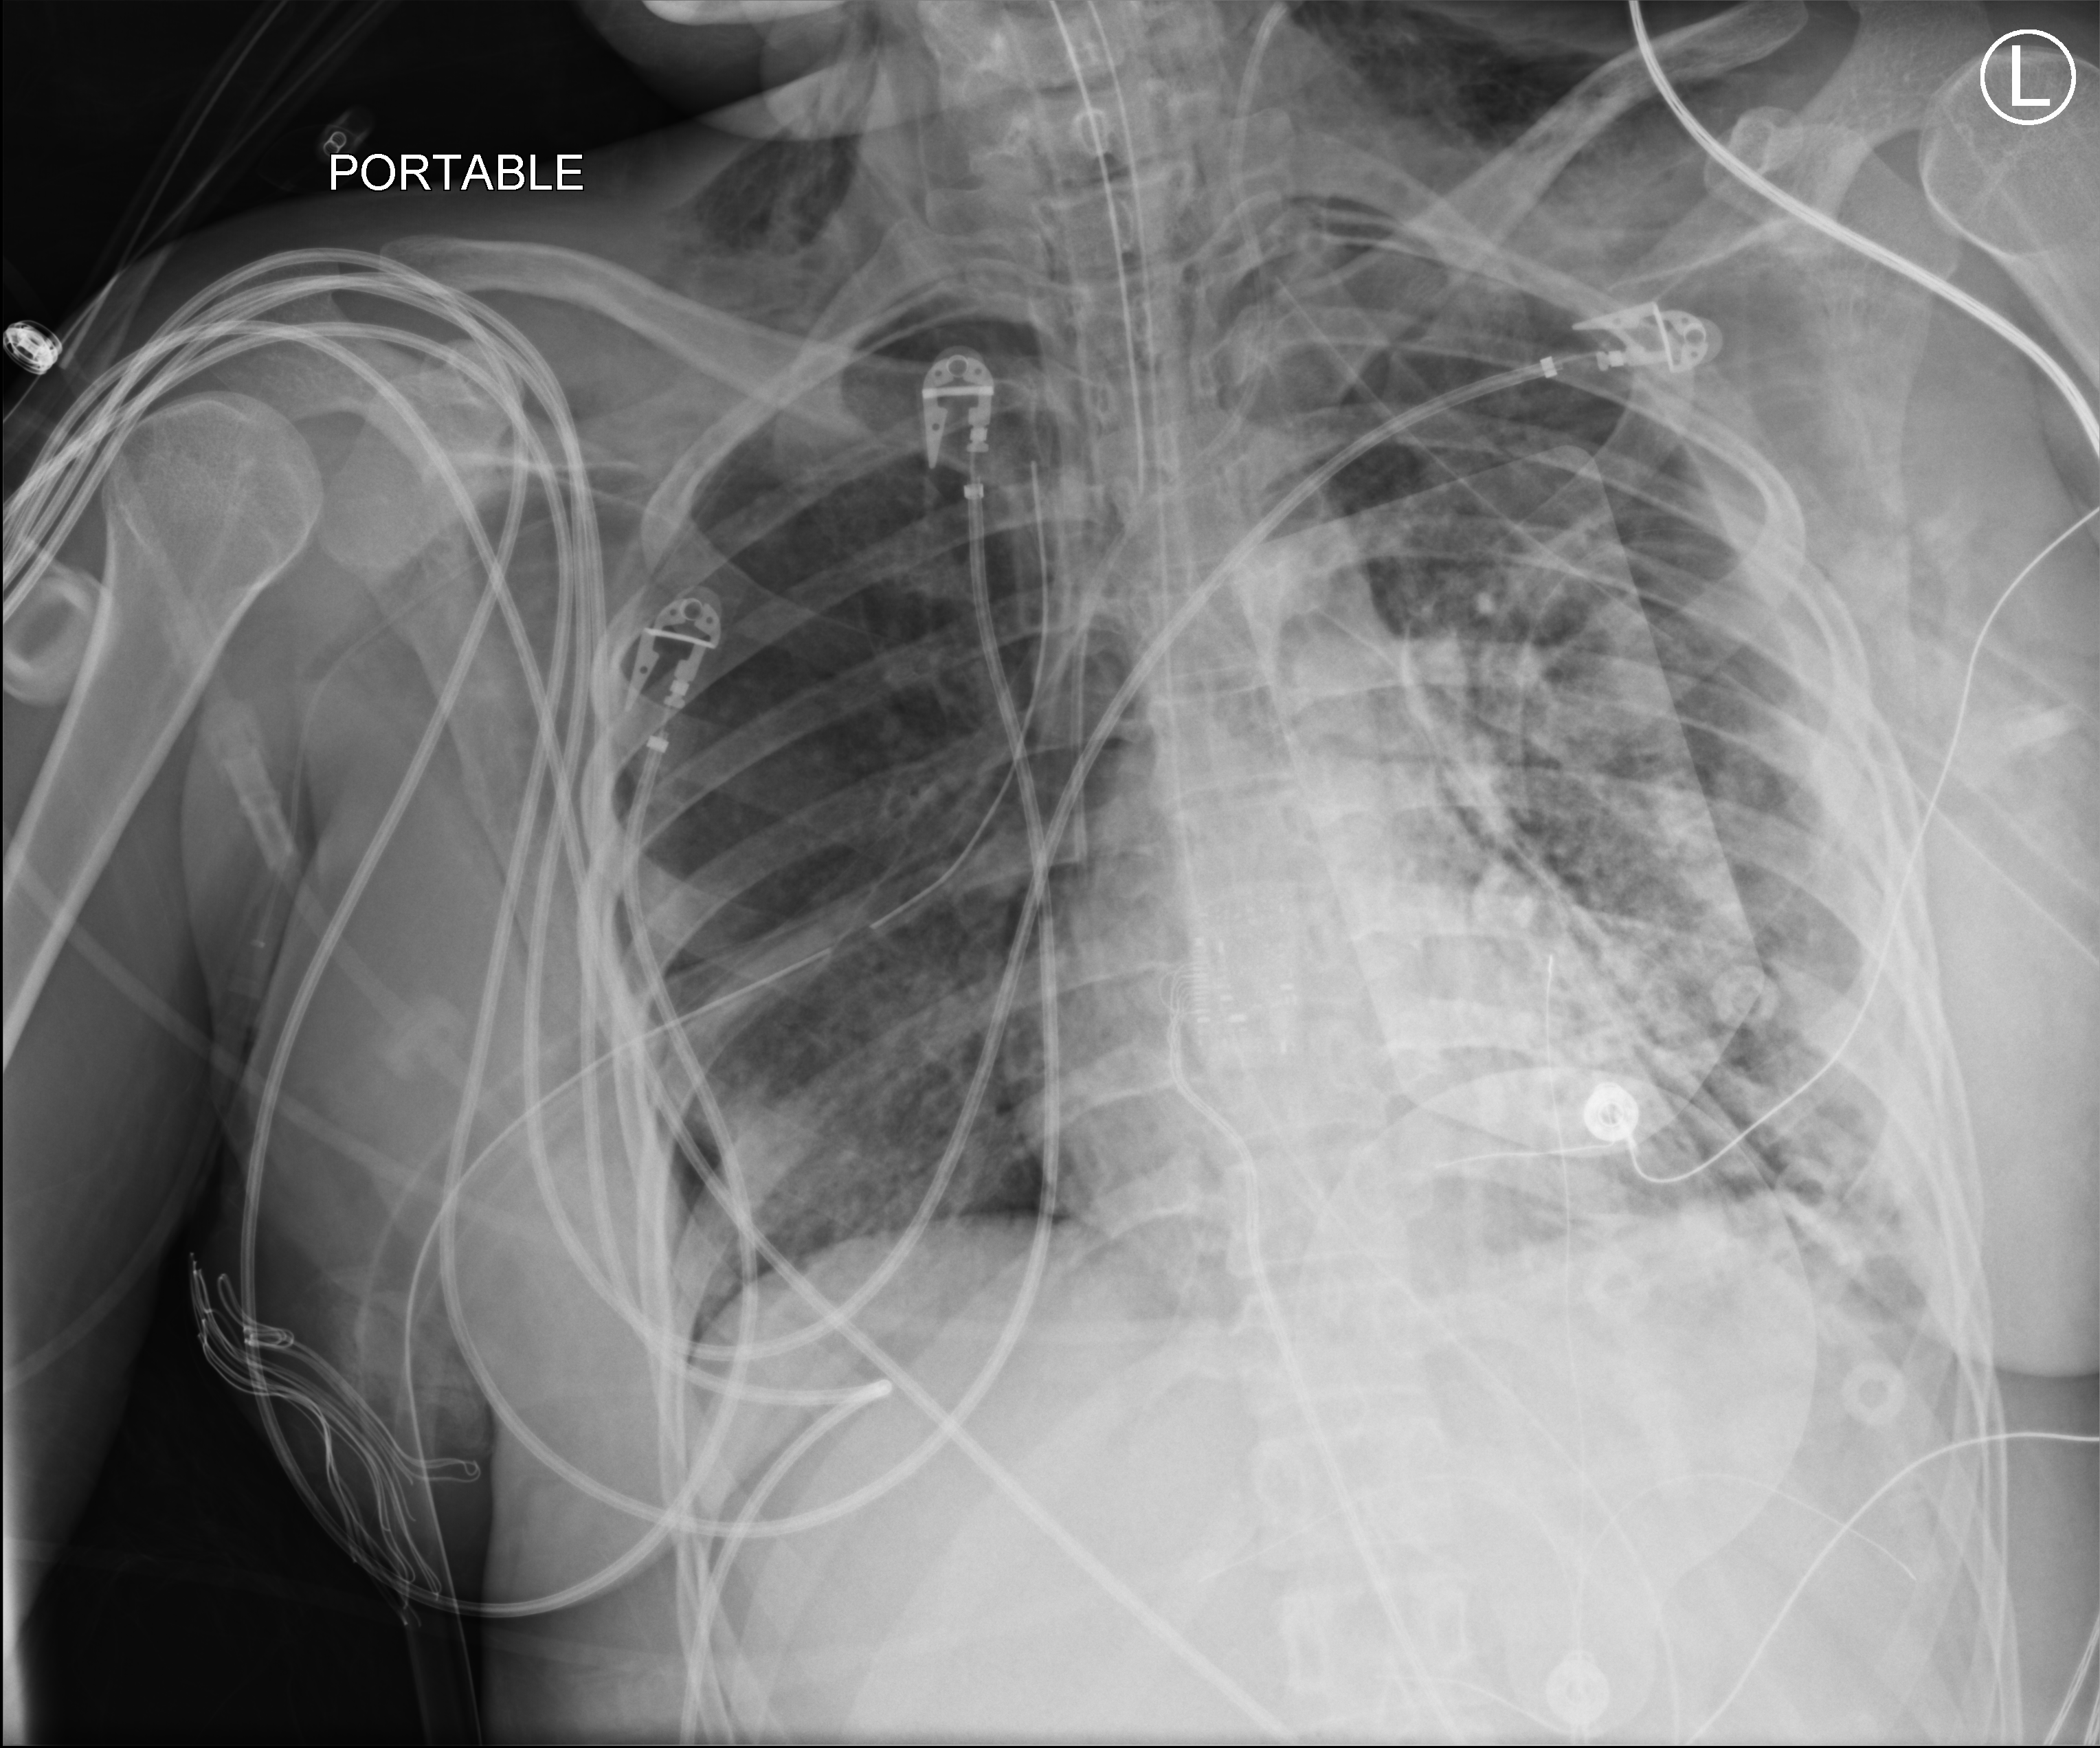
Portable chest radiograph. Patient hospitalised with COVID-19, aged 18–59 years.
Hospital-stay facts (about this admission, not read from this image; timing relative to this image not recorded): chronic kidney disease (admission record): no; COPD (admission record): no; diabetes (admission record): no.